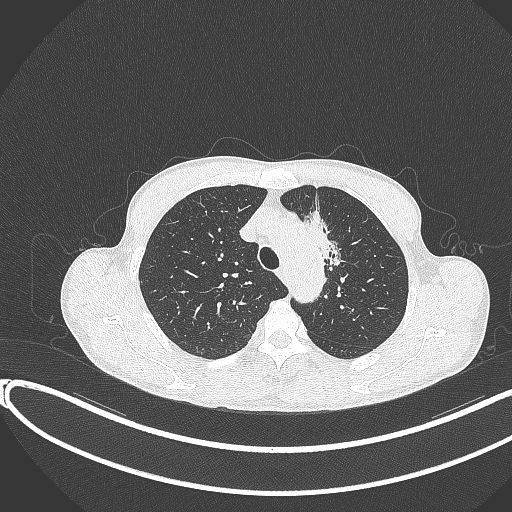
Chest CT, one axial slice; position 293 of 374 along the scan axis; reconstruction kernel B70f; lung window (W 1500 / L -600 HU); 1 mm slice thickness; 512 × 512 image matrix. Male patient, age 58 years. Case-level facts recorded for this patient, not image findings: clinical TNM (as recorded): T1c N1 M0.
Annotated regions visible in this slice (bounding box drawn by a radiologist):
- lung tumour (recorded histology: adenocarcinoma): bounding box <297,209,344,271> (left, top, right, bottom; pixels)